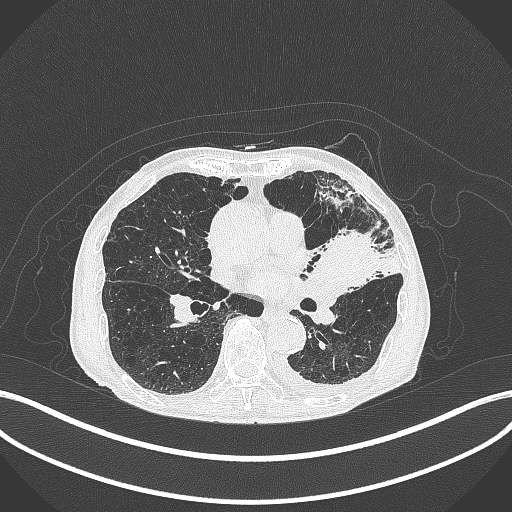
Chest CT, one axial slice; position 190 of 385 along the scan axis; reconstruction kernel B70f; 120 kVp; lung window (W 1500 / L -600 HU); 1 mm slice thickness; 512 × 512 image matrix, field of view 400 × 400 mm. Patient: male, 90 years or older. From the clinical record (not read from this slice): clinical TNM (as recorded): T2b N1 M0.
Structures marked on this image (rectangle marked by the reading radiologist):
- lung tumour (recorded histology: squamous cell carcinoma): bounding box (x1, y1, x2, y2) in pixels: (308, 226, 382, 291)